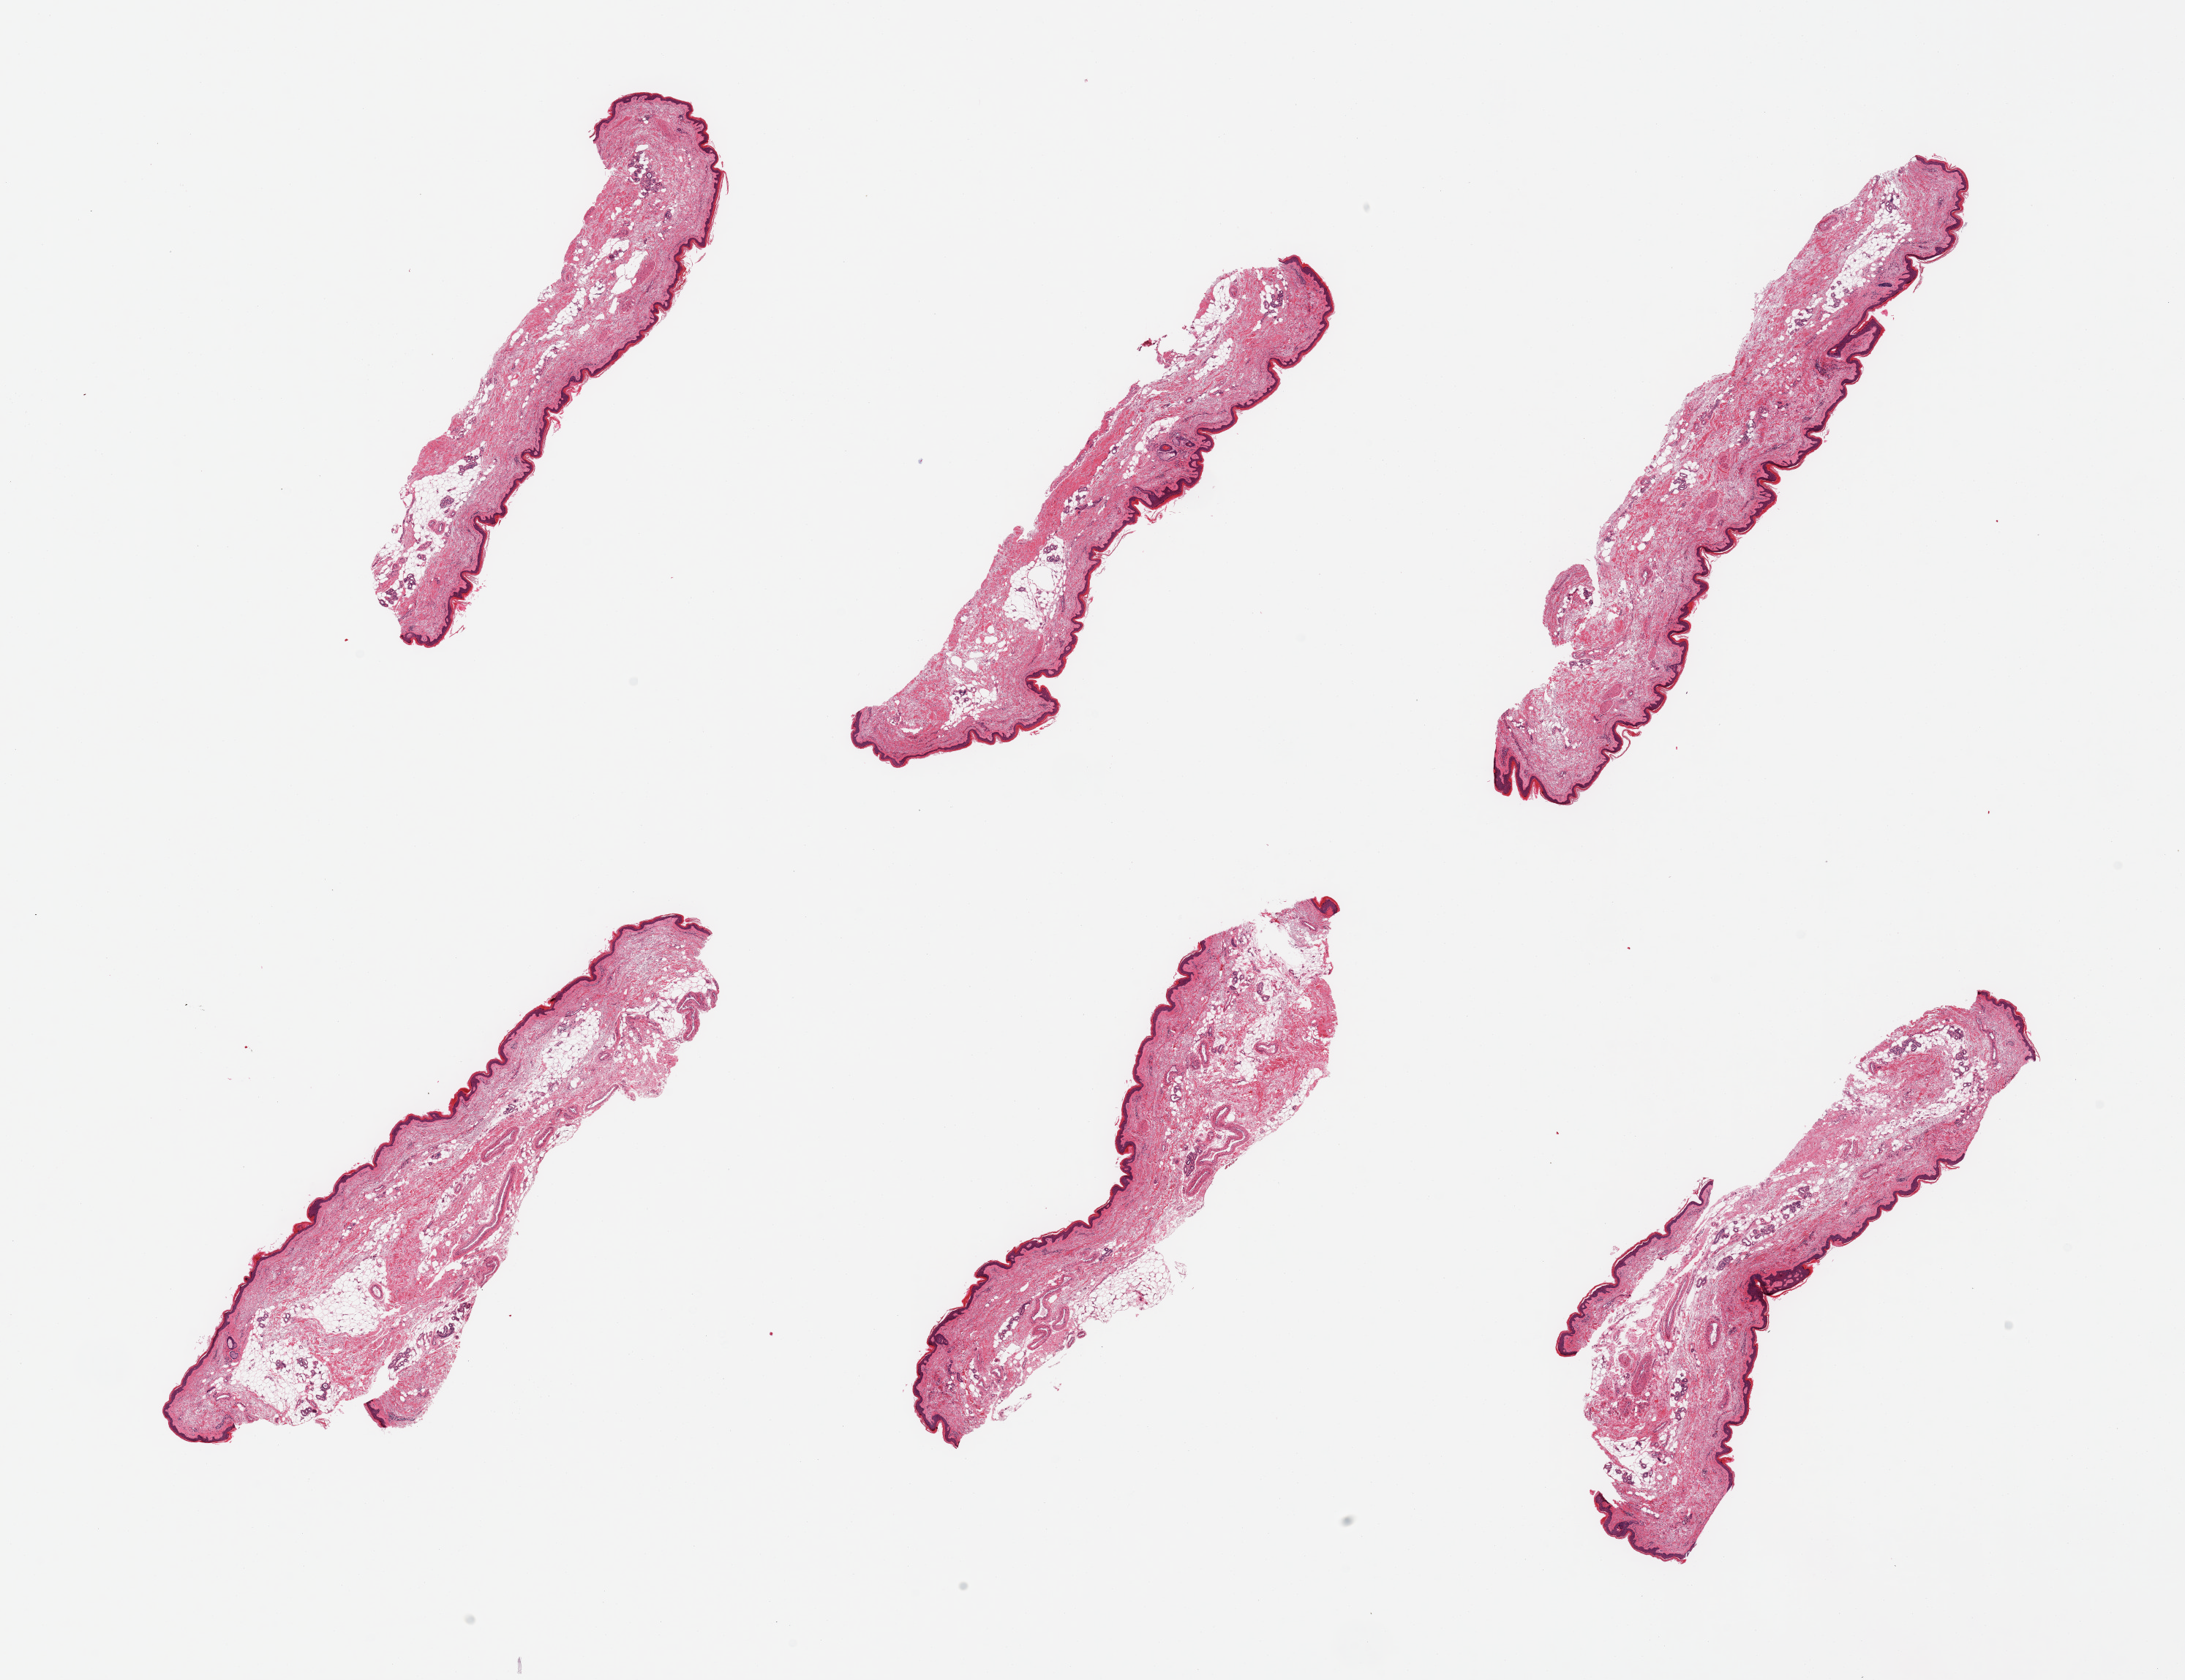
H&E whole-slide image — whole scanned area (about 23.6 x 18.2 mm, slide scanned at 20x) shown as a low-resolution overview; PAXgene-fixed, paraffin-embedded tissue; section of skin of lower leg (target tissue); tissue donor sample. Female donor.
Review note (as recorded): 6 pieces; well trimmed; 20% dermal fat.